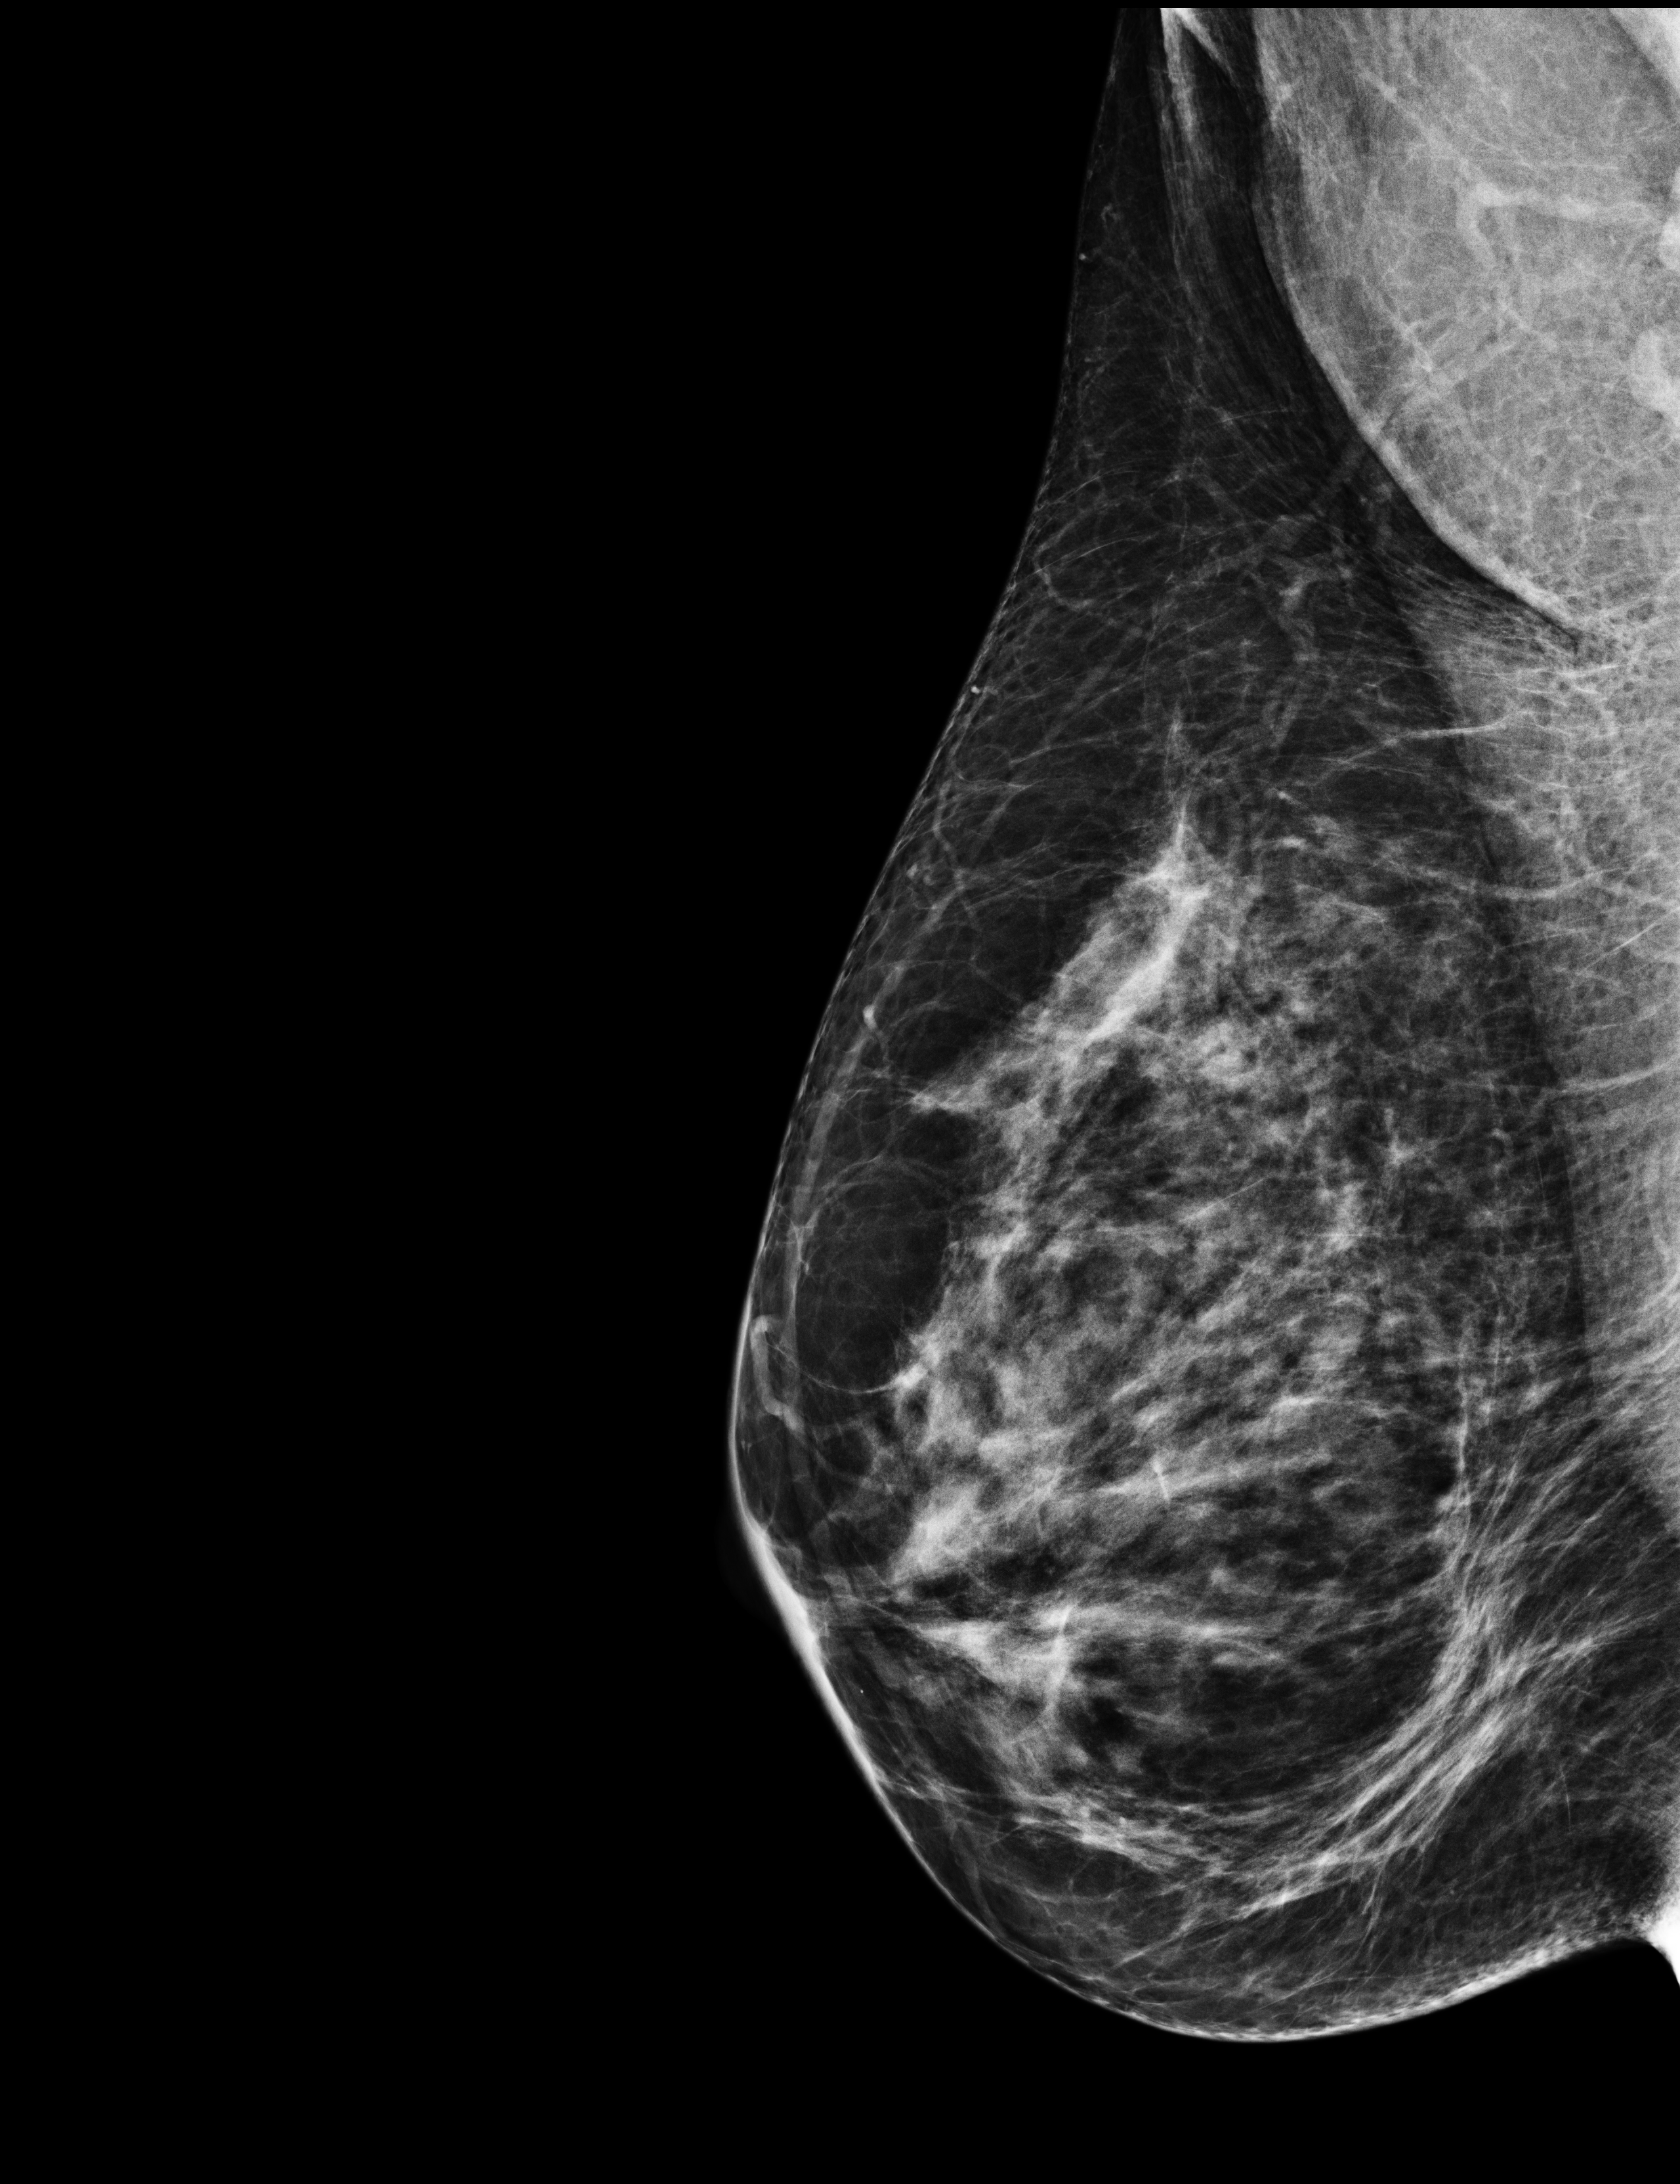
Annual screening mammography examination; compressed breast thickness 57 mm.
Image type: full-field digital mammogram. Breast: right. Projection: medio-lateral oblique projection.